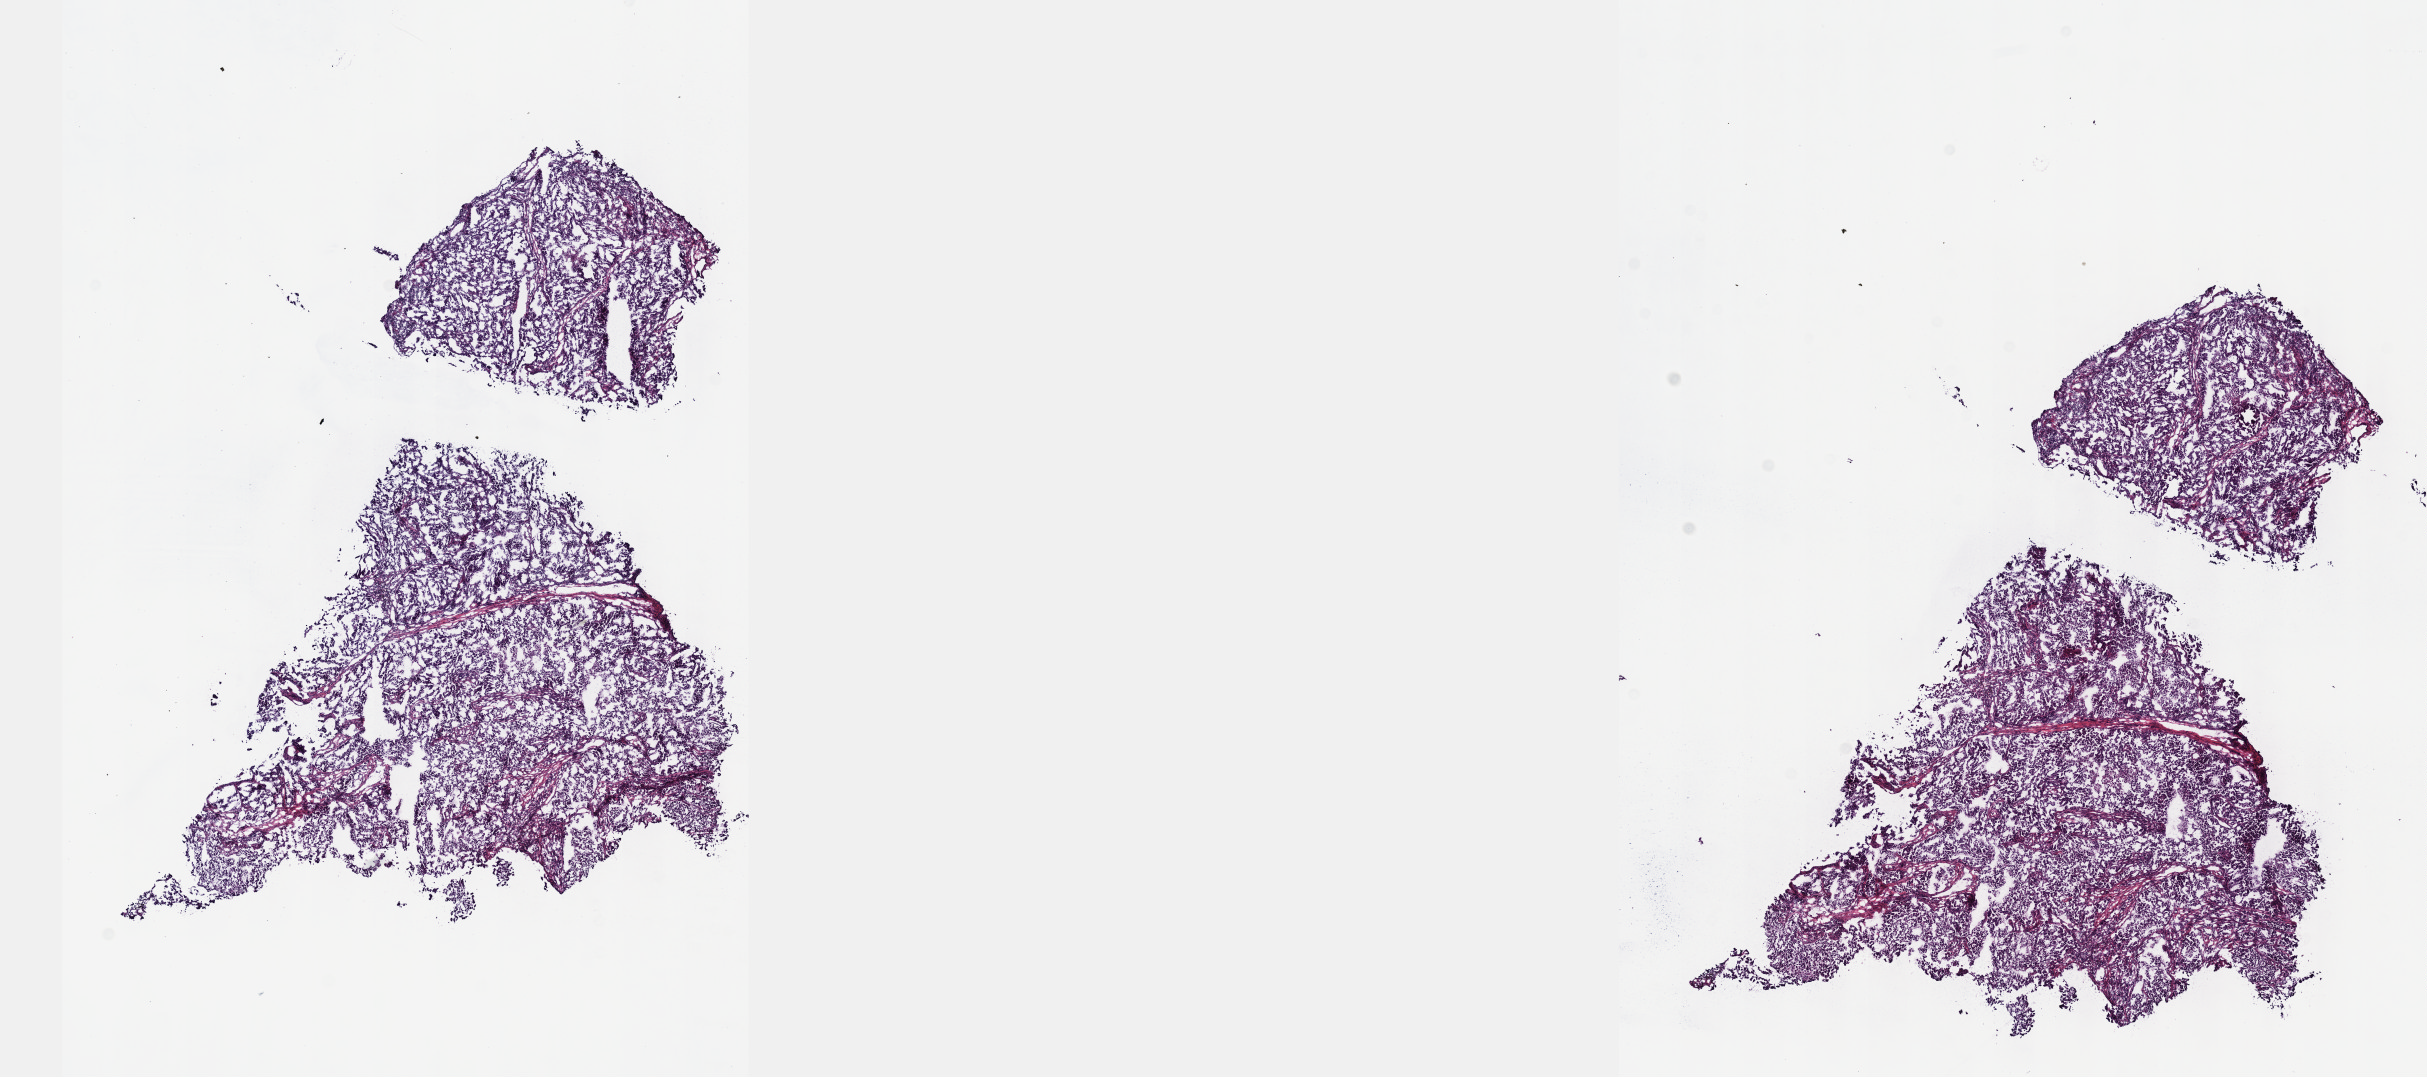
Digitized Hematoxylin and eosin (H&E) stained tissue section (whole slide) — a low-resolution overview of the entire scanned area, about 19.6 x 8.7 mm, frozen section, primary tumour sample from the lung. Female patient; age at initial diagnosis 41 years. Pathologist review of this section (percent, as recorded): tumour cells 80%, tumour nuclei 80%, normal cells 0%, stromal cells 20%, necrosis 0%. Infiltration values recorded for this section: lymphocyte infiltration 2%, monocyte infiltration 1%, neutrophil infiltration 5%.
AJCC pathologic stage: I. Pathologic diagnosis: Adenocarcinoma, NOS (upper lobe, lung).